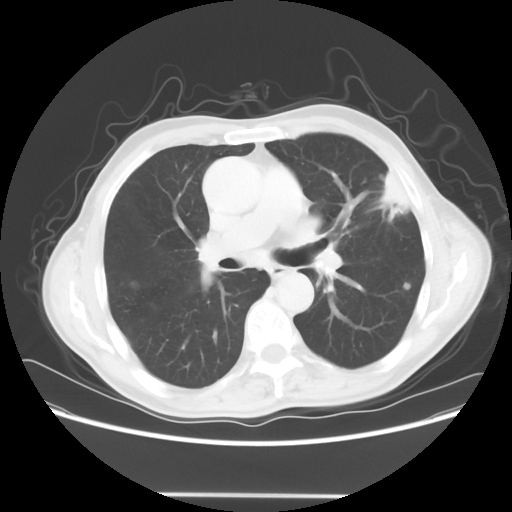
Chest CT, one axial slice; slice 37 of 64 in the series (ordered by position); reconstruction kernel STANDARD; 120 kVp; lung window (W 1500 / L -600 HU); 512 × 512 image matrix, field of view 392 × 392 mm. Patient: male, 71 years. Case-level facts recorded for this patient, not image findings: clinical TNM (as recorded): T1c N0 M0; histopathological grade: G2-3.
Annotated regions visible in this slice (rectangle marked by the reading radiologist):
- lung tumour (recorded histology: adenocarcinoma): box from (x=371, y=161) to (x=411, y=215) px